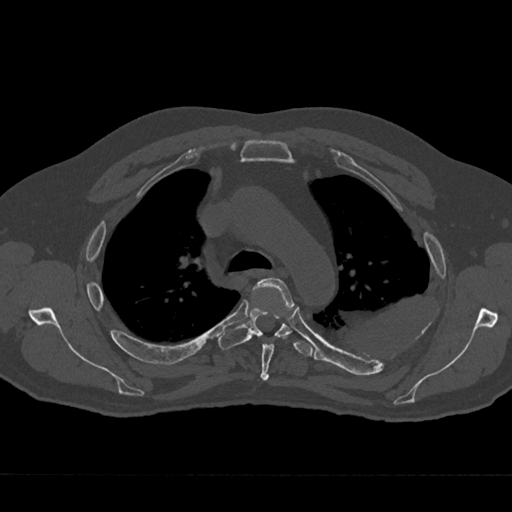
CT including the spine, one axial slice; position 496 of 797 along the scan axis; bone window (W 1800 / L 400 HU); 0.5 mm slice thickness; 512 × 512 image matrix, field of view 377 × 377 mm. Male patient, age 75 years. Case-level facts recorded for this patient, not image findings: primary cancer: renal; vertebrae with lytic lesions (as recorded): T4.
Annotated regions visible in this slice (semi-automatic segmentation, software-assisted and operator-edited):
- T4 vertebra: bounding box <253,278,294,381> (left, top, right, bottom; pixels)
- T5 vertebra: <218,298,313,356>